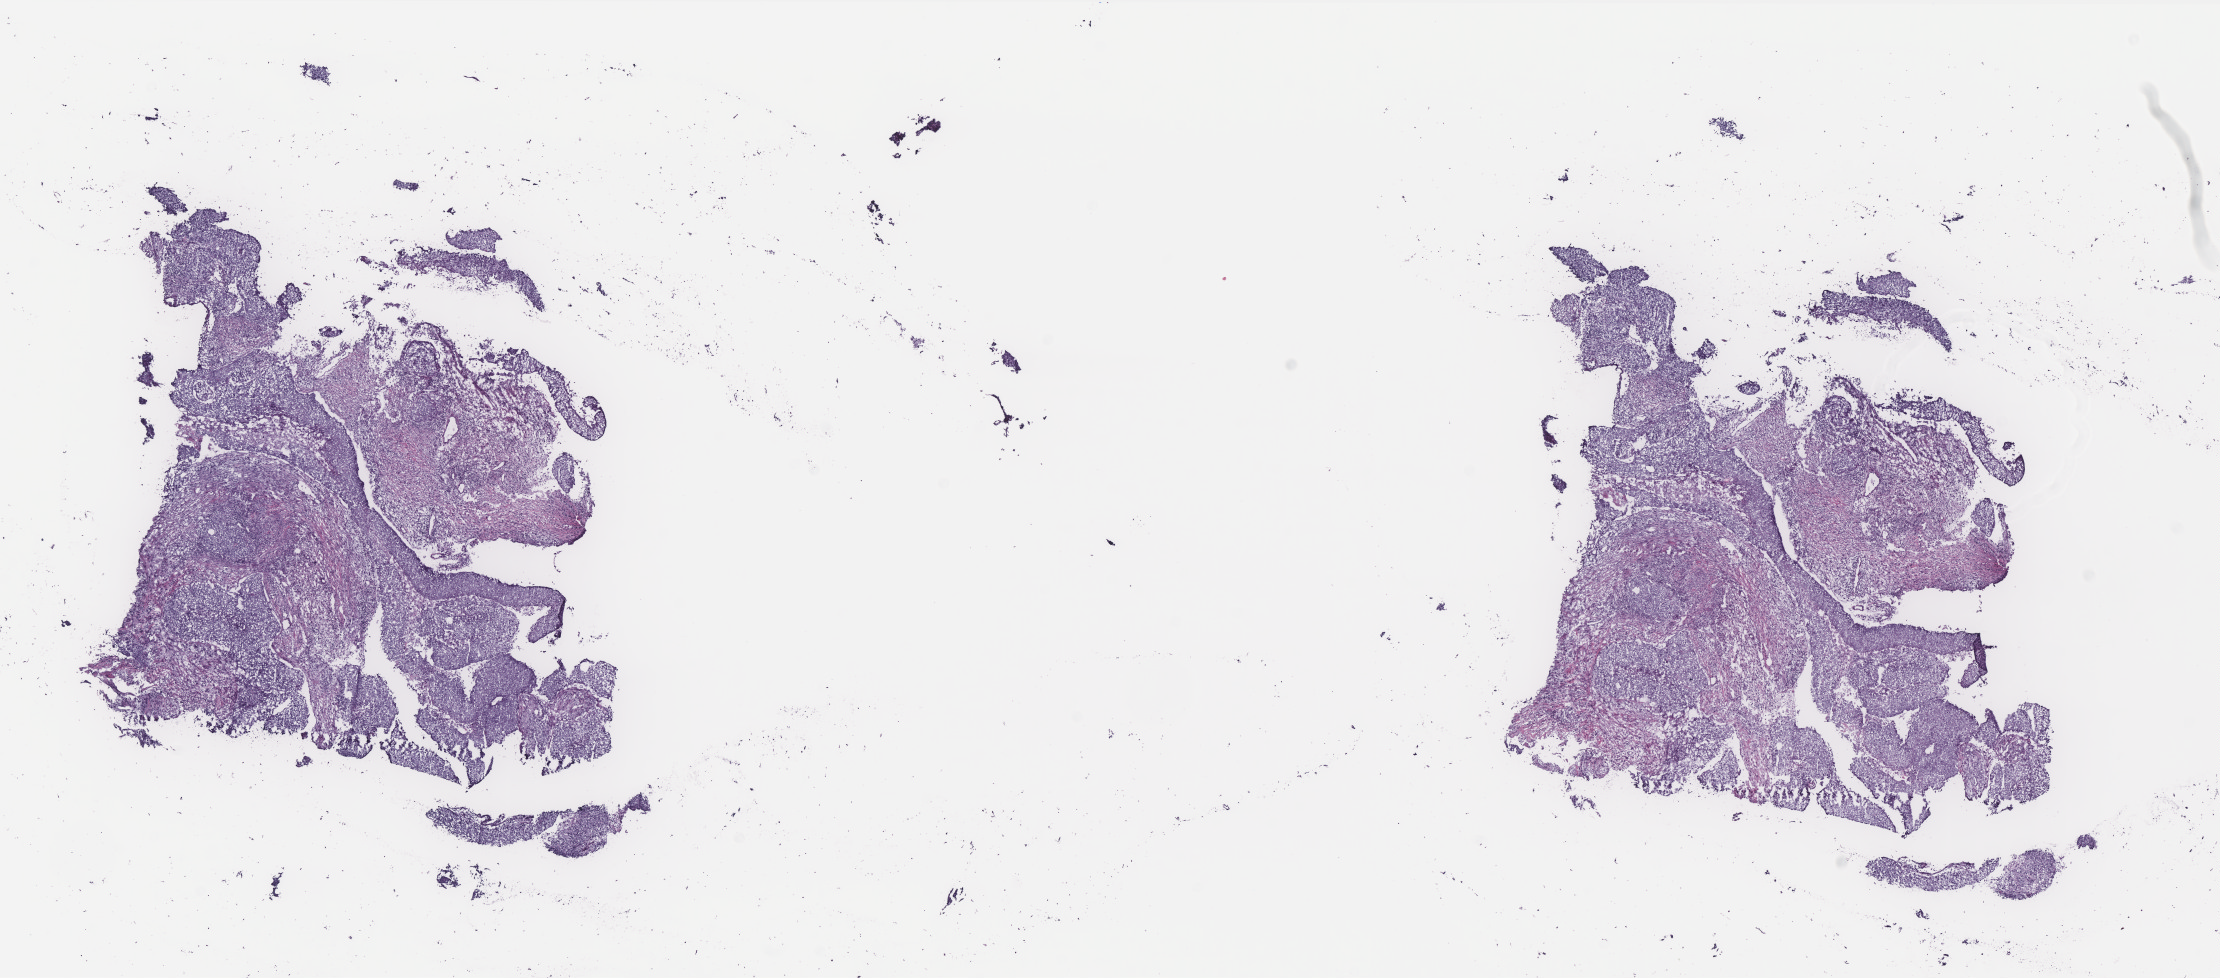
Whole-slide histology image, Hematoxylin and eosin (H&E) stained — low-resolution overview of the scanned area, about 17.8 x 7.8 mm (from a 40x scan), frozen section from the top of the tissue portion, cervix, primary tumour sample. Female, age 79 years at initial diagnosis. Histologic grade: G3 (poorly differentiated). Composition of this section per pathologist review: tumour cells 80%, tumour nuclei 80%, normal cells 0%, stromal cells 10%, necrosis 10%. Infiltration values recorded for this section: lymphocyte infiltration 40%, monocyte infiltration 20%, neutrophil infiltration 20%.
FIGO stage: IIIB. Pathologic diagnosis: Squamous cell carcinoma, NOS (cervix uteri).